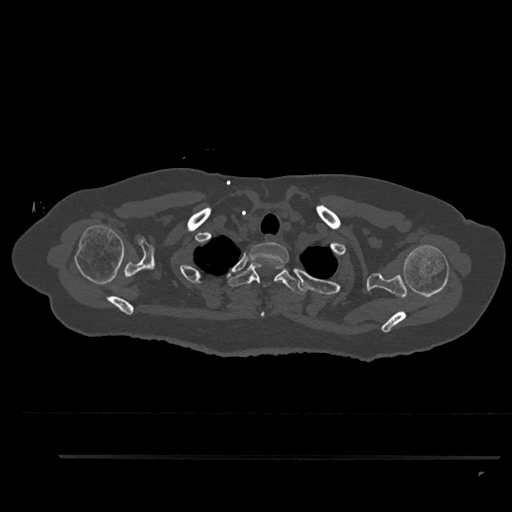
CT including the spine, one axial slice; slice 737 of 797 in the series (ordered by position); bone window (W 1800 / L 400 HU); 512 × 512 image matrix, field of view 408 × 408 mm. Female patient, age 44 years. Case-level facts recorded for this patient, not image findings: primary cancer: renal.
Annotated regions visible in this slice (semi-automatic segmentation, software-assisted and operator-edited):
- T1 vertebra: box from (x=249, y=242) to (x=289, y=317) px
- T2 vertebra: (x=227, y=263)–(x=307, y=295)